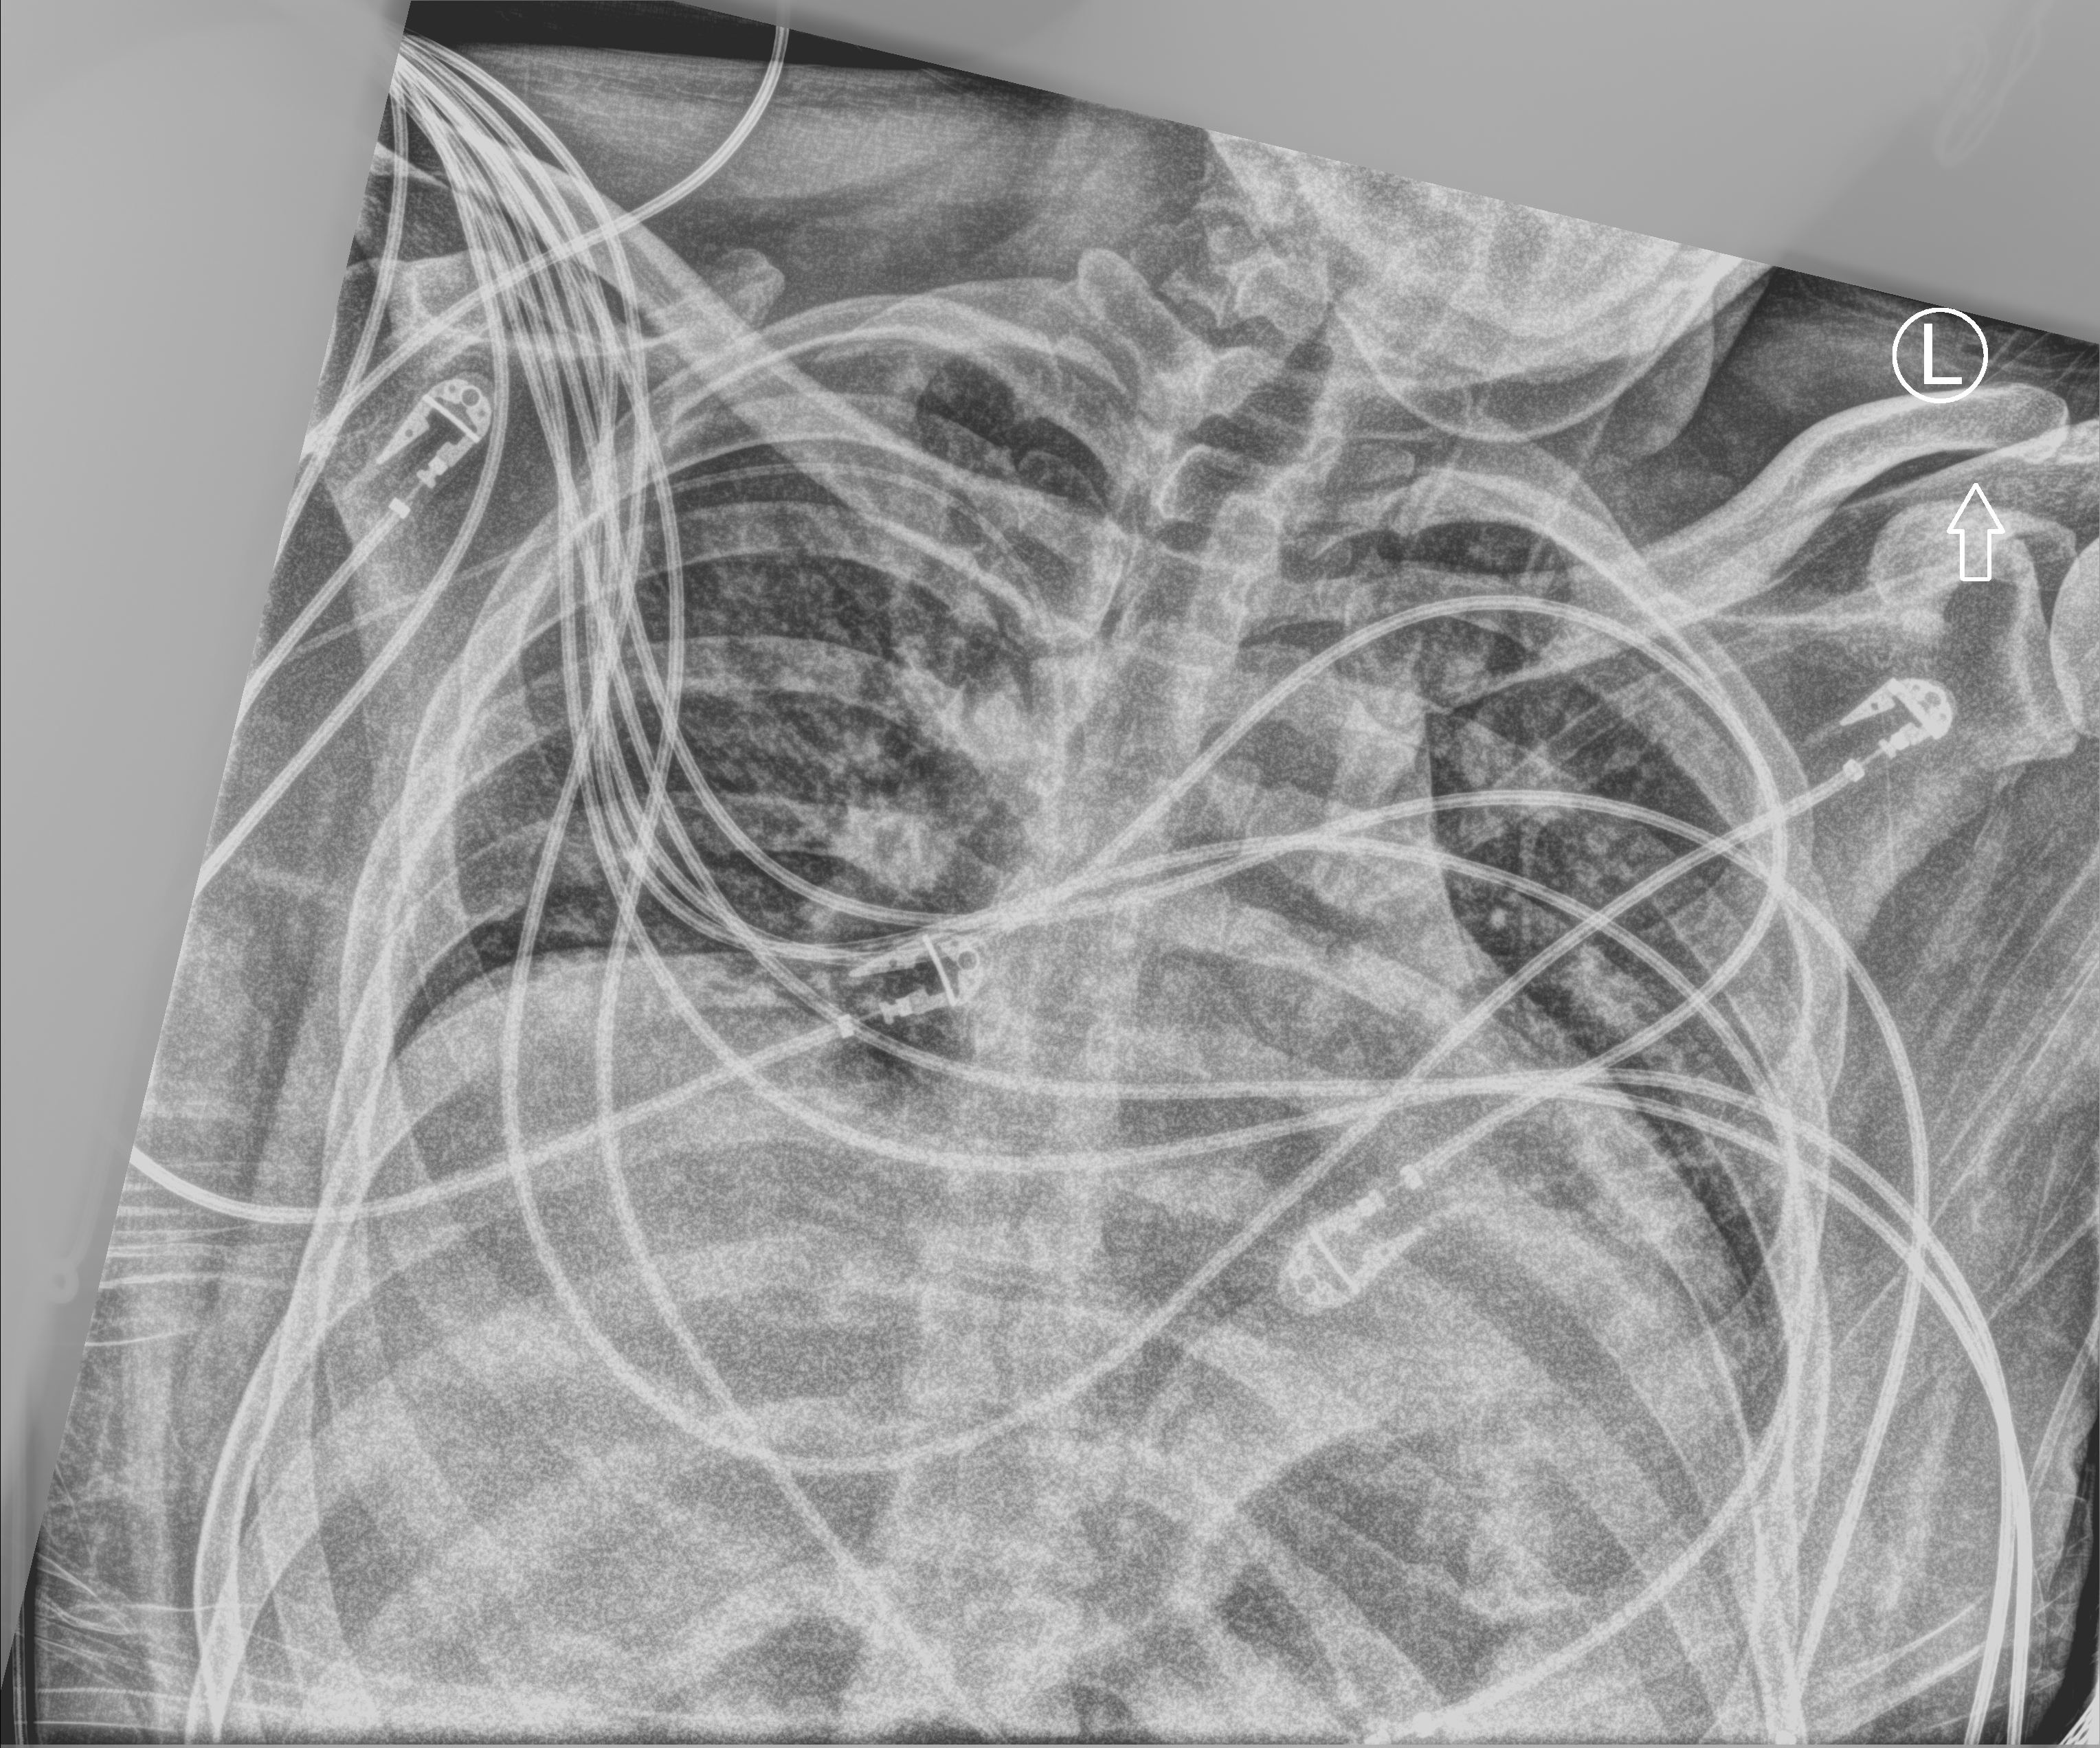
Portable chest radiograph; anteroposterior (AP) projection. Male patient hospitalised with COVID-19, age 18–59 years.
Admission-level facts for this patient (not findings on this image; timing relative to this image not recorded):
- mechanically ventilated during this hospital stay: yes
- admitted to intensive care during this hospital stay: no